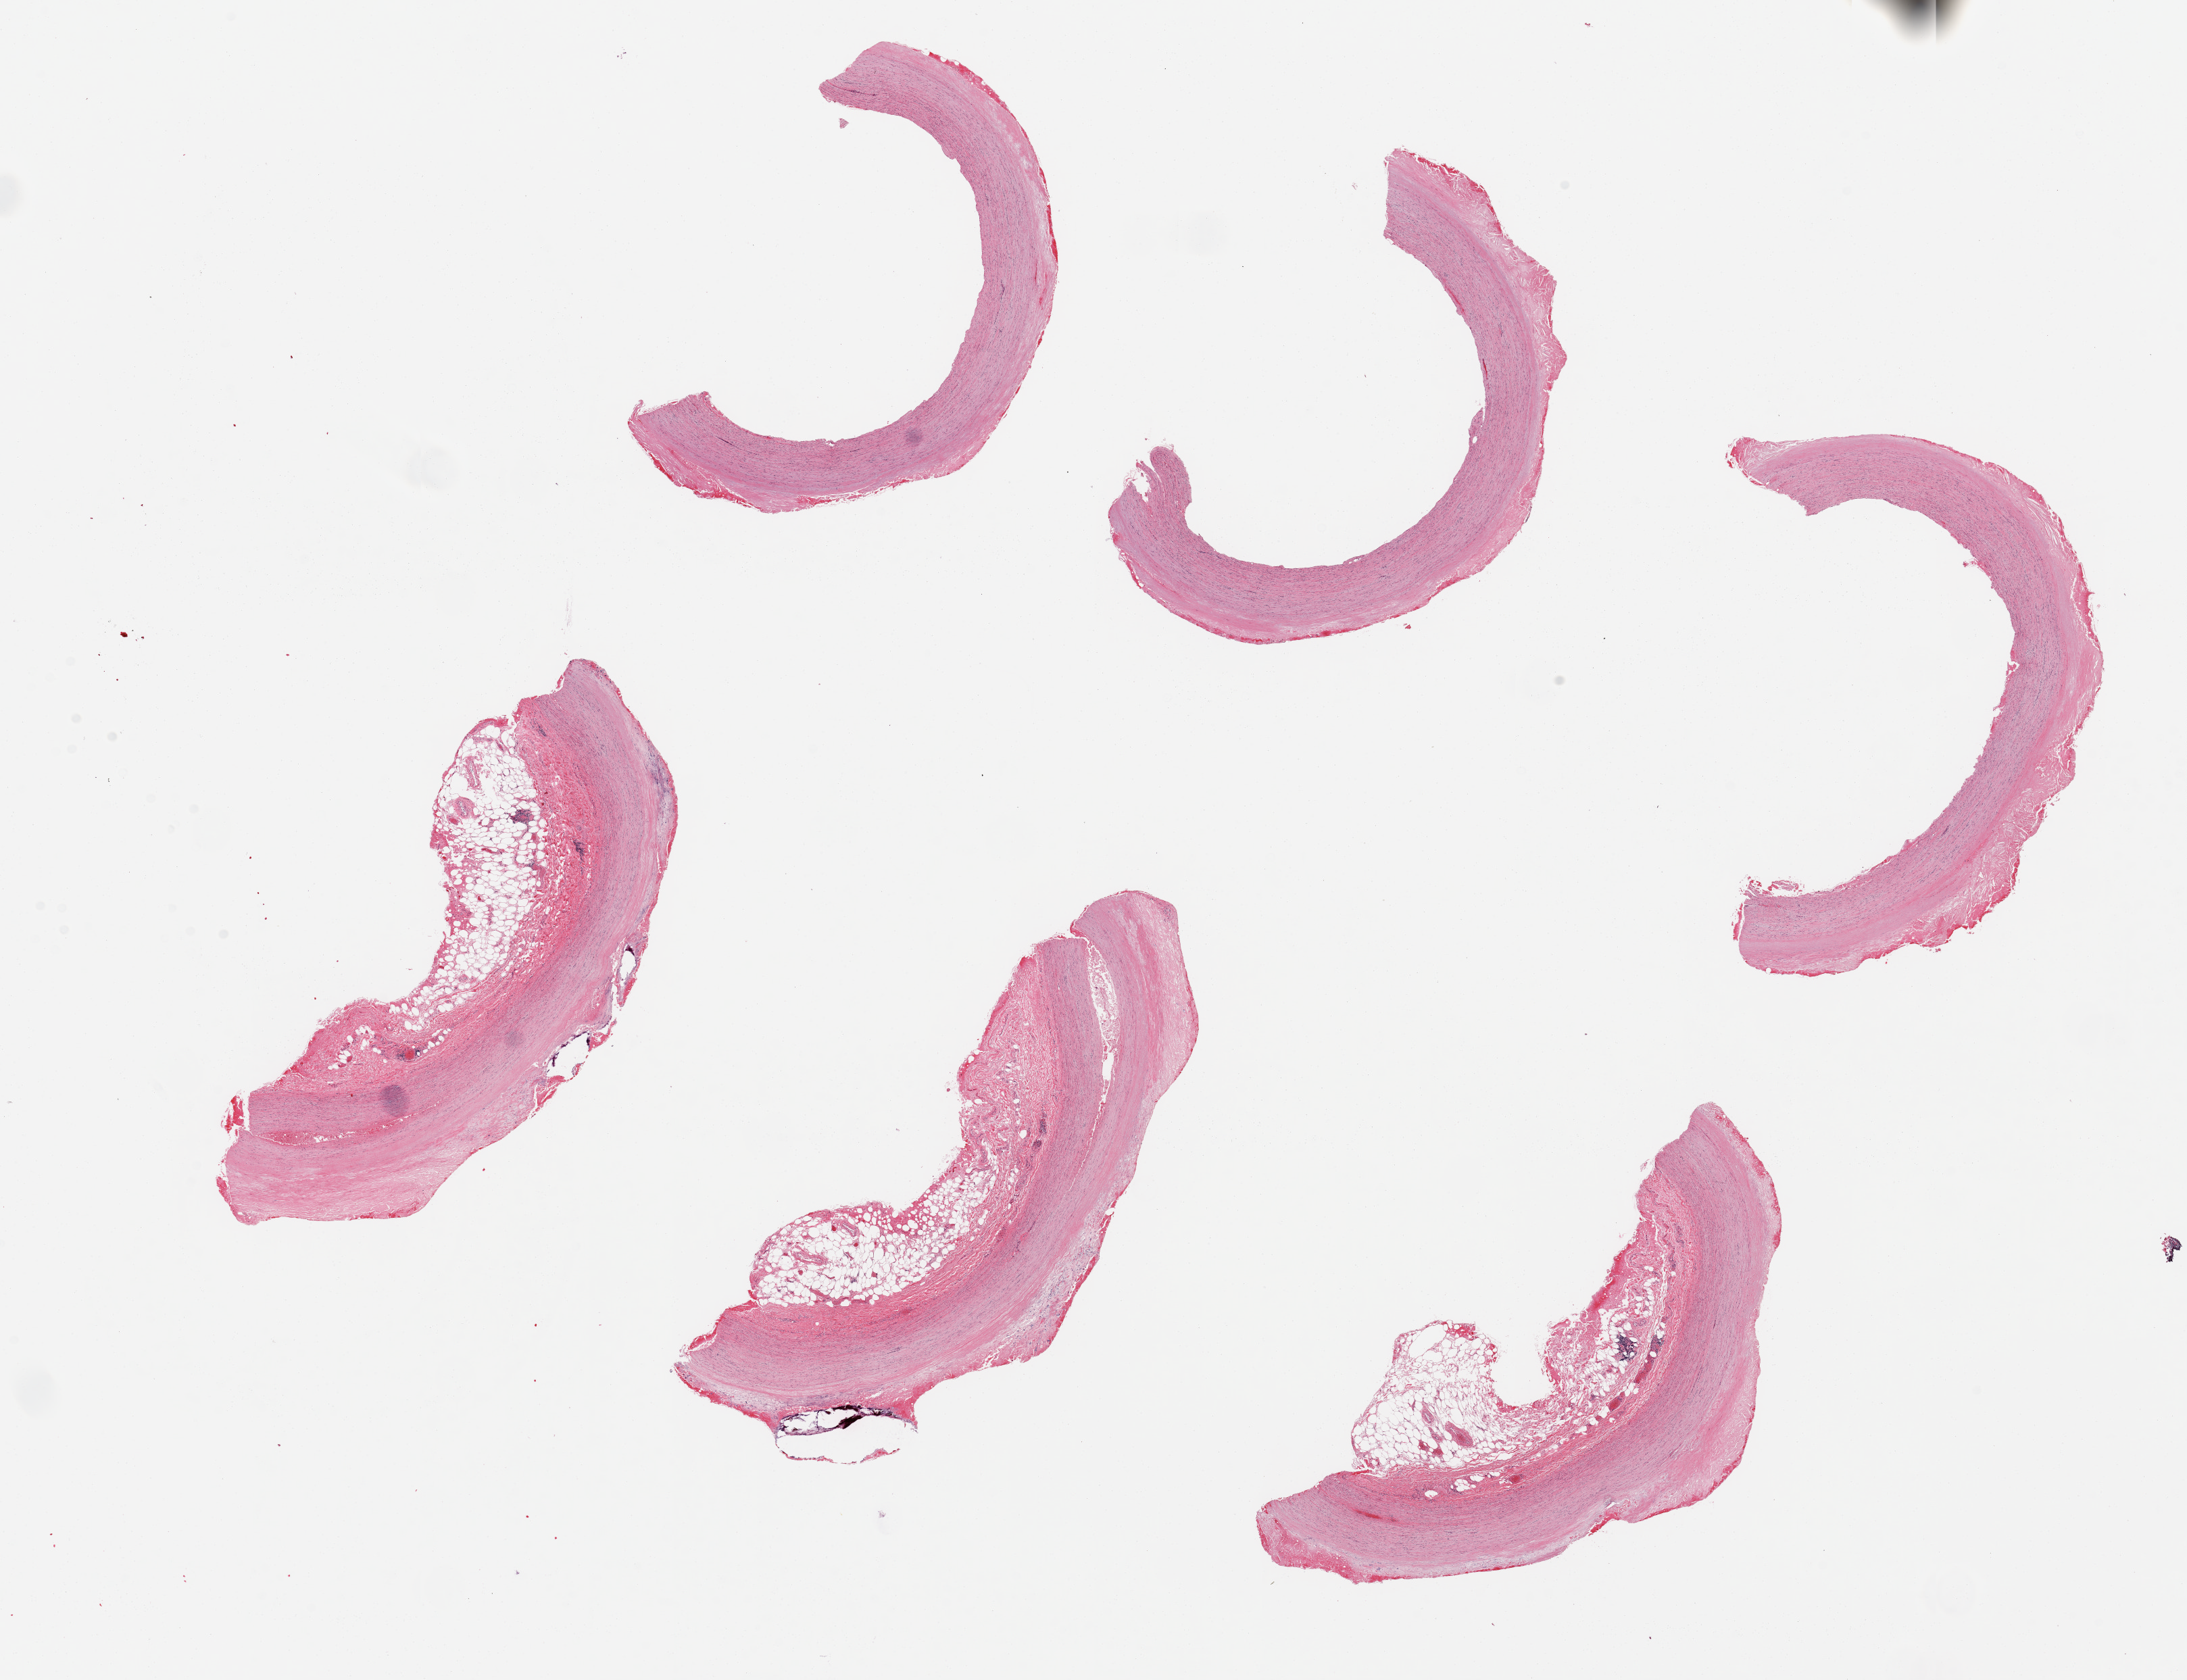
Whole-slide image, haematoxylin and eosin stain, brightfield, low-resolution overview of the scanned area, about 25.6 x 19.7 mm (acquisition: 20x scan), PAXgene-fixed paraffin-embedded (PFPE) section, section of aorta (target tissue), donor tissue sample. Male donor.
Pathologist's review note for this sample: 6 pieces, atherosclerotic deposits up to ~0.5mm, adherent fat/serosa up to ~1mm, several sections.